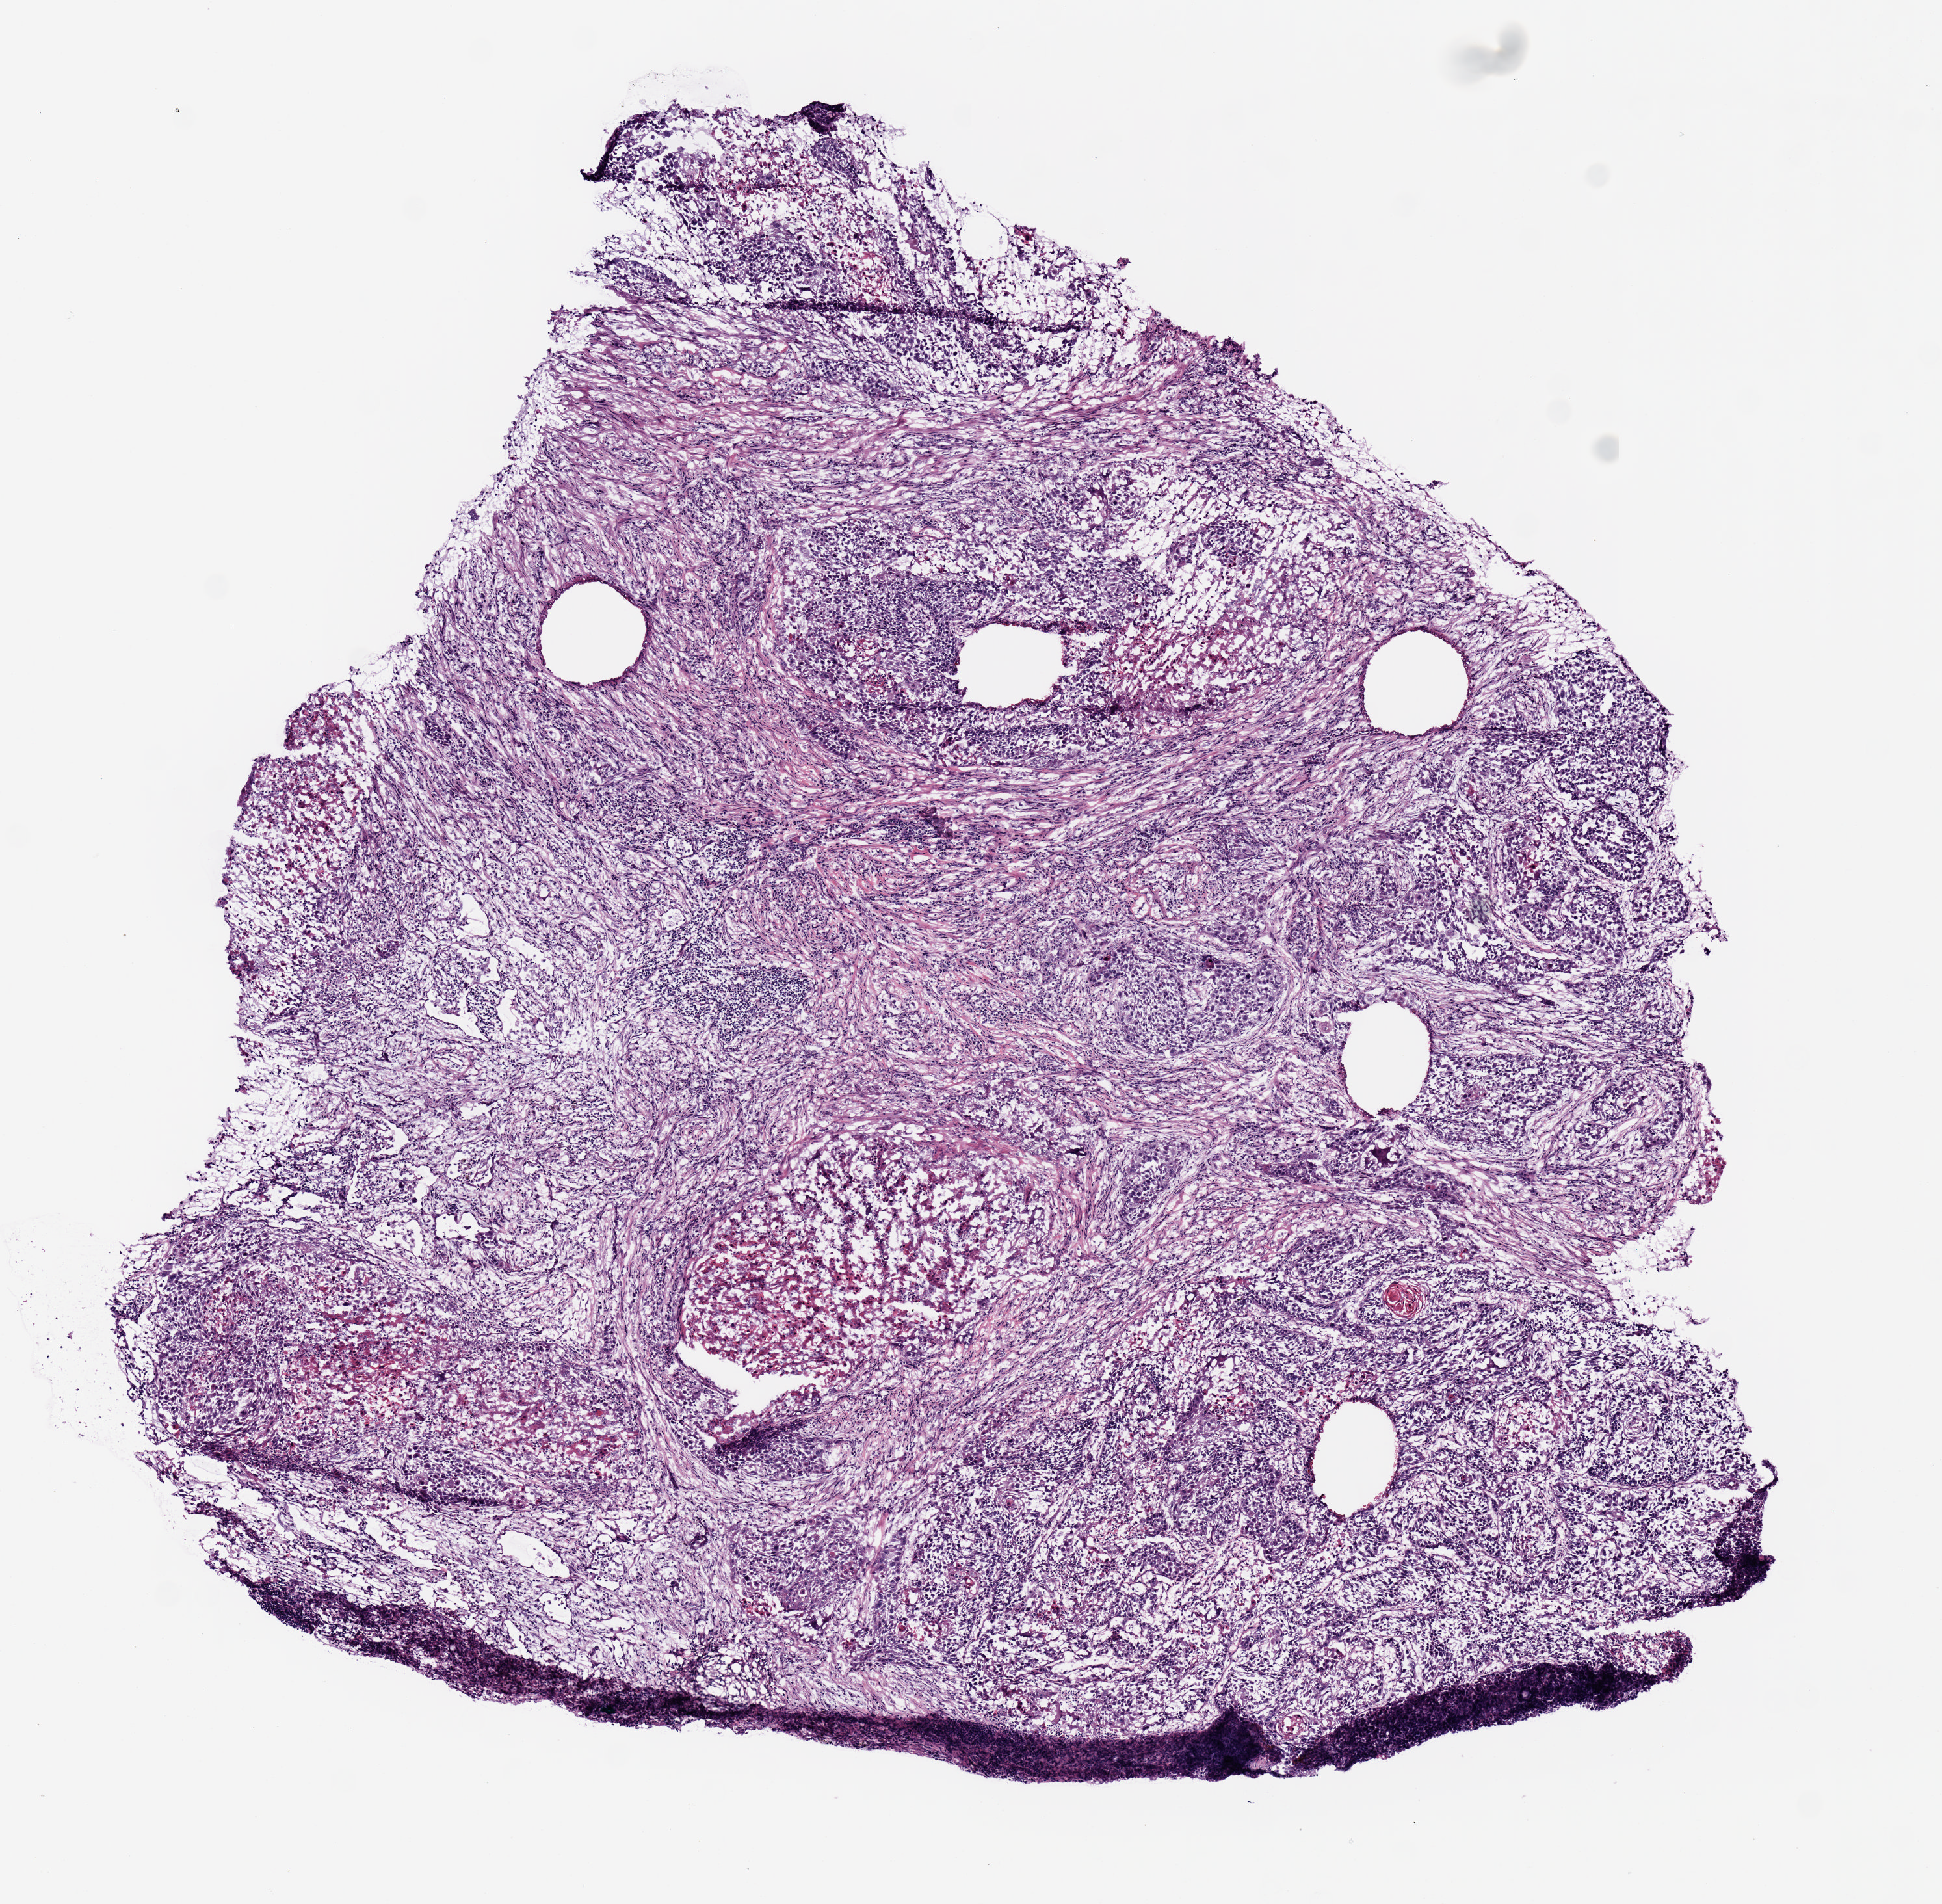
H&E whole-slide image — a low-resolution overview of the entire scanned area, about 5.9 x 5.8 mm, frozen section from the top of the tissue portion, primary tumour sample from the lung. Male, age 61 years at initial diagnosis. Slide review estimates, as recorded: tumour cells 90%, tumour nuclei 70%, normal cells 0%, stromal cells 10%, necrosis 0%.
Diagnosis: Squamous cell carcinoma, NOS (upper lobe, lung). Laterality: left. AJCC pathologic stage: IIIA (7th edition). TNM: T3 N1 M0.